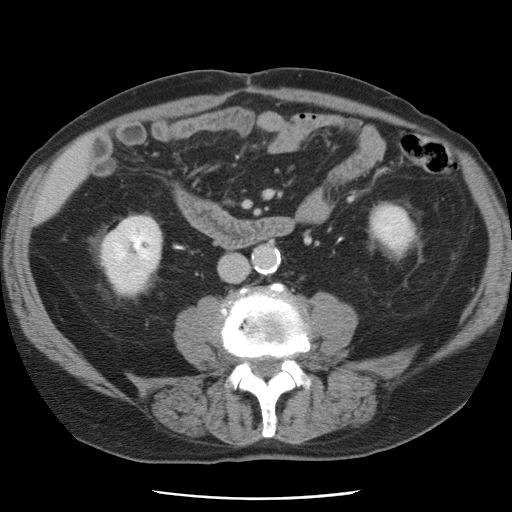
Contrast-enhanced abdominal CT, one axial slice. Slice 13 of 78 in the series (ordered by position). Intravenous contrast given. Soft-tissue window (W 400 / L 40 HU). 512 × 512 image matrix, field of view 337 × 337 mm. Male patient, age 75 years. From the clinical record (not read from this slice): diagnosis: colorectal cancer liver metastases, imaged before liver resection; multiple liver metastases: yes; largest metastasis: 2.4 cm.
Structures marked on this image (manually delineated by an expert):
- liver: box from (x=37, y=143) to (x=89, y=220) px
- planned liver remnant (the part of the liver to remain after resection): (x=36, y=142)–(x=90, y=220)